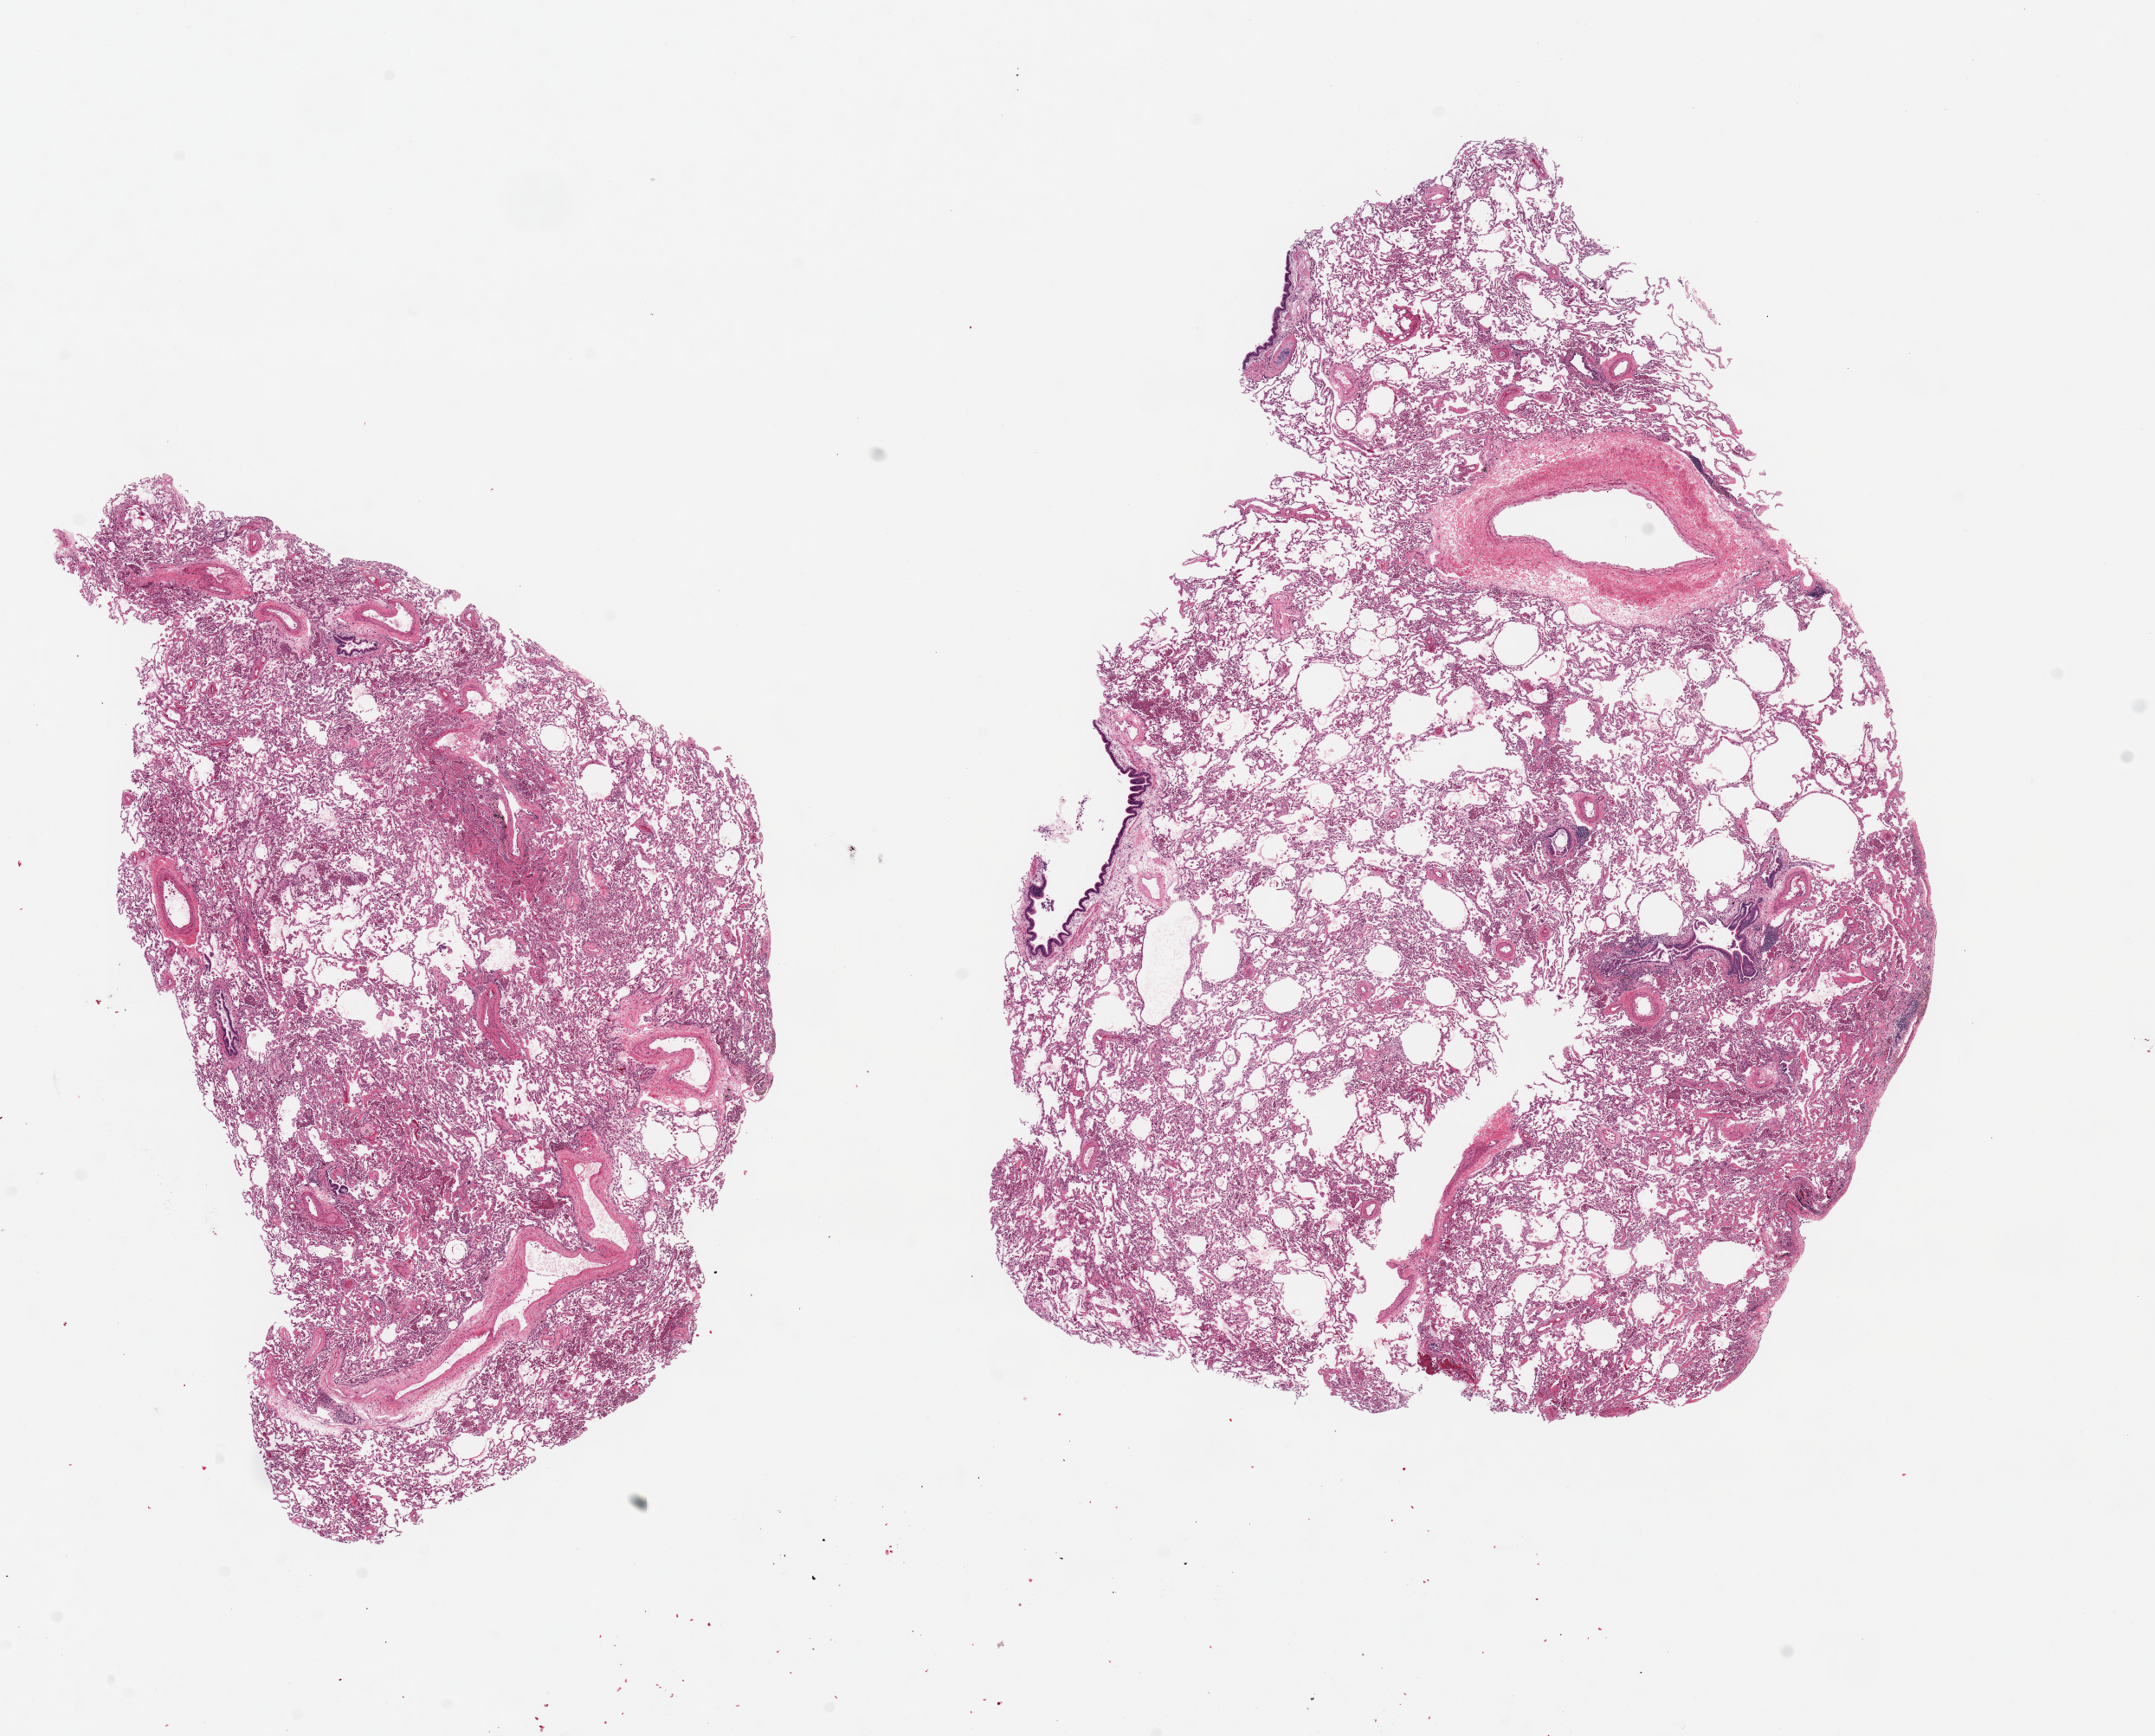
Whole-slide image, hematoxylin and eosin (H&E) stain, brightfield — shown as a low-resolution overview of the whole scanned area (about 19.7 x 15.9 mm, slide scanned at 20x), PAXgene-fixed paraffin-embedded (PFPE) section, target tissue: lung, donor tissue sample. Donor sex: male.
* review note (as recorded): 2 pieces, 10x6 & 12x9mm; Moderate numbers of heart failure cells